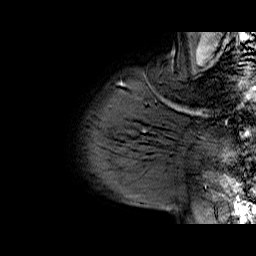
Breast MRI (dynamic contrast-enhanced), one sagittal slice. Slice 58 of 70 in the series (ordered by position). Dynamic contrast-enhanced series, time point 2 of 6 at this slice position (early post-contrast). 1.5 T. TE 6.5 ms, TR 33 ms. 4 mm slice thickness. 256 × 256 image matrix, field of view 200 × 200 mm. Female patient. Case-level facts recorded for this patient, not image findings: setting: breast cancer imaged before/during neoadjuvant chemotherapy; receptor status: HER2-positive.
Outlined on this slice (semi-automatic segmentation, software-assisted and operator-edited):
- analysis volume of interest (the breast-tissue region the enhancement analysis was run in; not a lesion): bounding box <113,112,174,170> (left, top, right, bottom; pixels)
- tumour enhancement mask (voxels above the 100 % enhancement threshold inside the analysis volume of interest): <143,130,146,132>